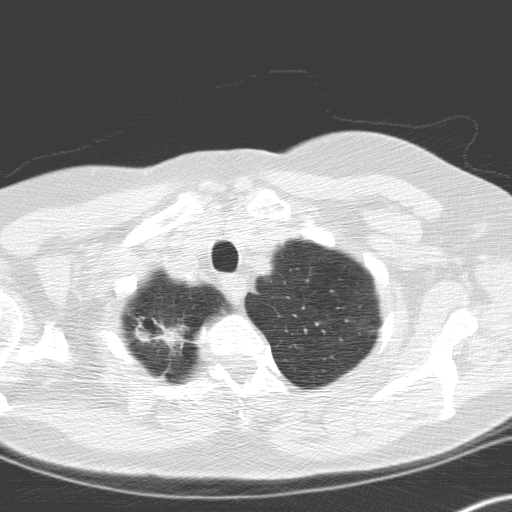
Axial slice from a low-dose chest CT screening exam. Second screening round (one year after baseline). Lung window (W 1500 / L -600 HU). Slice 24 of 166 in the series. 512 × 512 image matrix, field of view 306 × 306 mm. Female, age 60 years at enrolment.
Lesion marked by an expert reader, bounding box (x1, y1, x2, y2) in pixels: (127, 307, 202, 374). Screening reader's record for this exam (one nodule recorded; not confirmed to be the boxed lesion): non-calcified nodule or mass ≥4 mm, right upper lobe, 12 × 8 mm, spiculated (stellate) margins, soft tissue attenuation, pre-existing on the prior screen: no. Later outcome: lung cancer diagnosed 58 days after this screen — squamous cell carcinoma, keratinizing, NOS, right upper lobe, moderately differentiated (G2), stage IA (AJCC 6th edition), 20 mm at pathology.